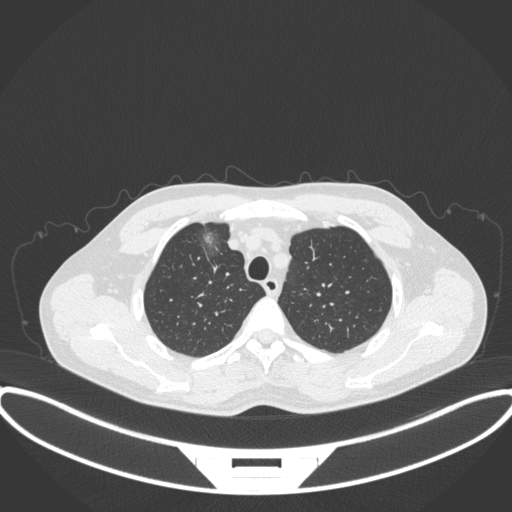
Chest CT, one axial slice. Position 296 of 395 along the scan axis. Reconstruction kernel B31f. Lung window (W 1500 / L -600 HU). 1 mm slice thickness. 512 × 512 image matrix. Male patient, age 60 years. From the clinical record (not read from this slice): clinical TNM (as recorded): T1c N0 M0.
Structures marked on this image (bounding box drawn by a radiologist):
- lung tumour (recorded histology: adenocarcinoma): bounding box <198,225,227,264> (left, top, right, bottom; pixels)